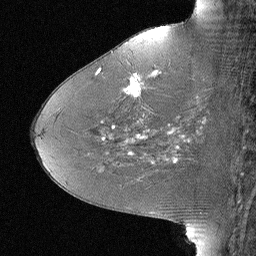
Breast MRI (dynamic contrast-enhanced), one sagittal slice. Position 29 of 64 along the scan axis. Dynamic contrast-enhanced study with each time point stored as its own series, time point 2 of 3 at this slice position (early post-contrast, ordered by acquisition time). 1.5 T. TE 4 ms, TR 30 ms. 2.25 mm slice thickness. 256 × 256 image matrix, field of view 180 × 180 mm. Female patient, age 46 years. Case-level facts recorded for this patient, not image findings: setting: breast cancer imaged before/during neoadjuvant chemotherapy; receptor status: HR-positive, HER2-negative.
Structures marked on this image (semi-automatically segmented with operator editing):
- analysis volume of interest (the breast-tissue region the enhancement analysis was run in; not a lesion): bounding box (x1, y1, x2, y2) in pixels: (106, 43, 184, 119)
- tumour enhancement mask (voxels above the 90 % enhancement threshold inside the analysis volume of interest): (124, 72, 157, 97)